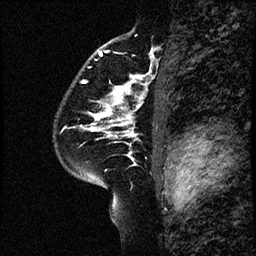
Breast MRI (dynamic contrast-enhanced), one sagittal slice. Position 42 of 60 along the scan axis. Dynamic contrast-enhanced study with each time point stored as its own series, time point 2 of 4 at this slice position (early post-contrast, ordered by acquisition time). 1.5 T. TE 4.2 ms, TR 17.6 ms. 2 mm slice thickness. 256 × 256 image matrix. Patient: female, 43 years. From the clinical record (not read from this slice): setting: breast cancer imaged before/during neoadjuvant chemotherapy.
Annotated regions visible in this slice (semi-automatically segmented with operator editing):
- analysis volume of interest (the breast-tissue region the enhancement analysis was run in; not a lesion): bounding box (x1, y1, x2, y2) in pixels: (57, 65, 168, 188)
- tumour enhancement mask (voxels above the 100 % enhancement threshold inside the analysis volume of interest): (88, 93, 133, 136)